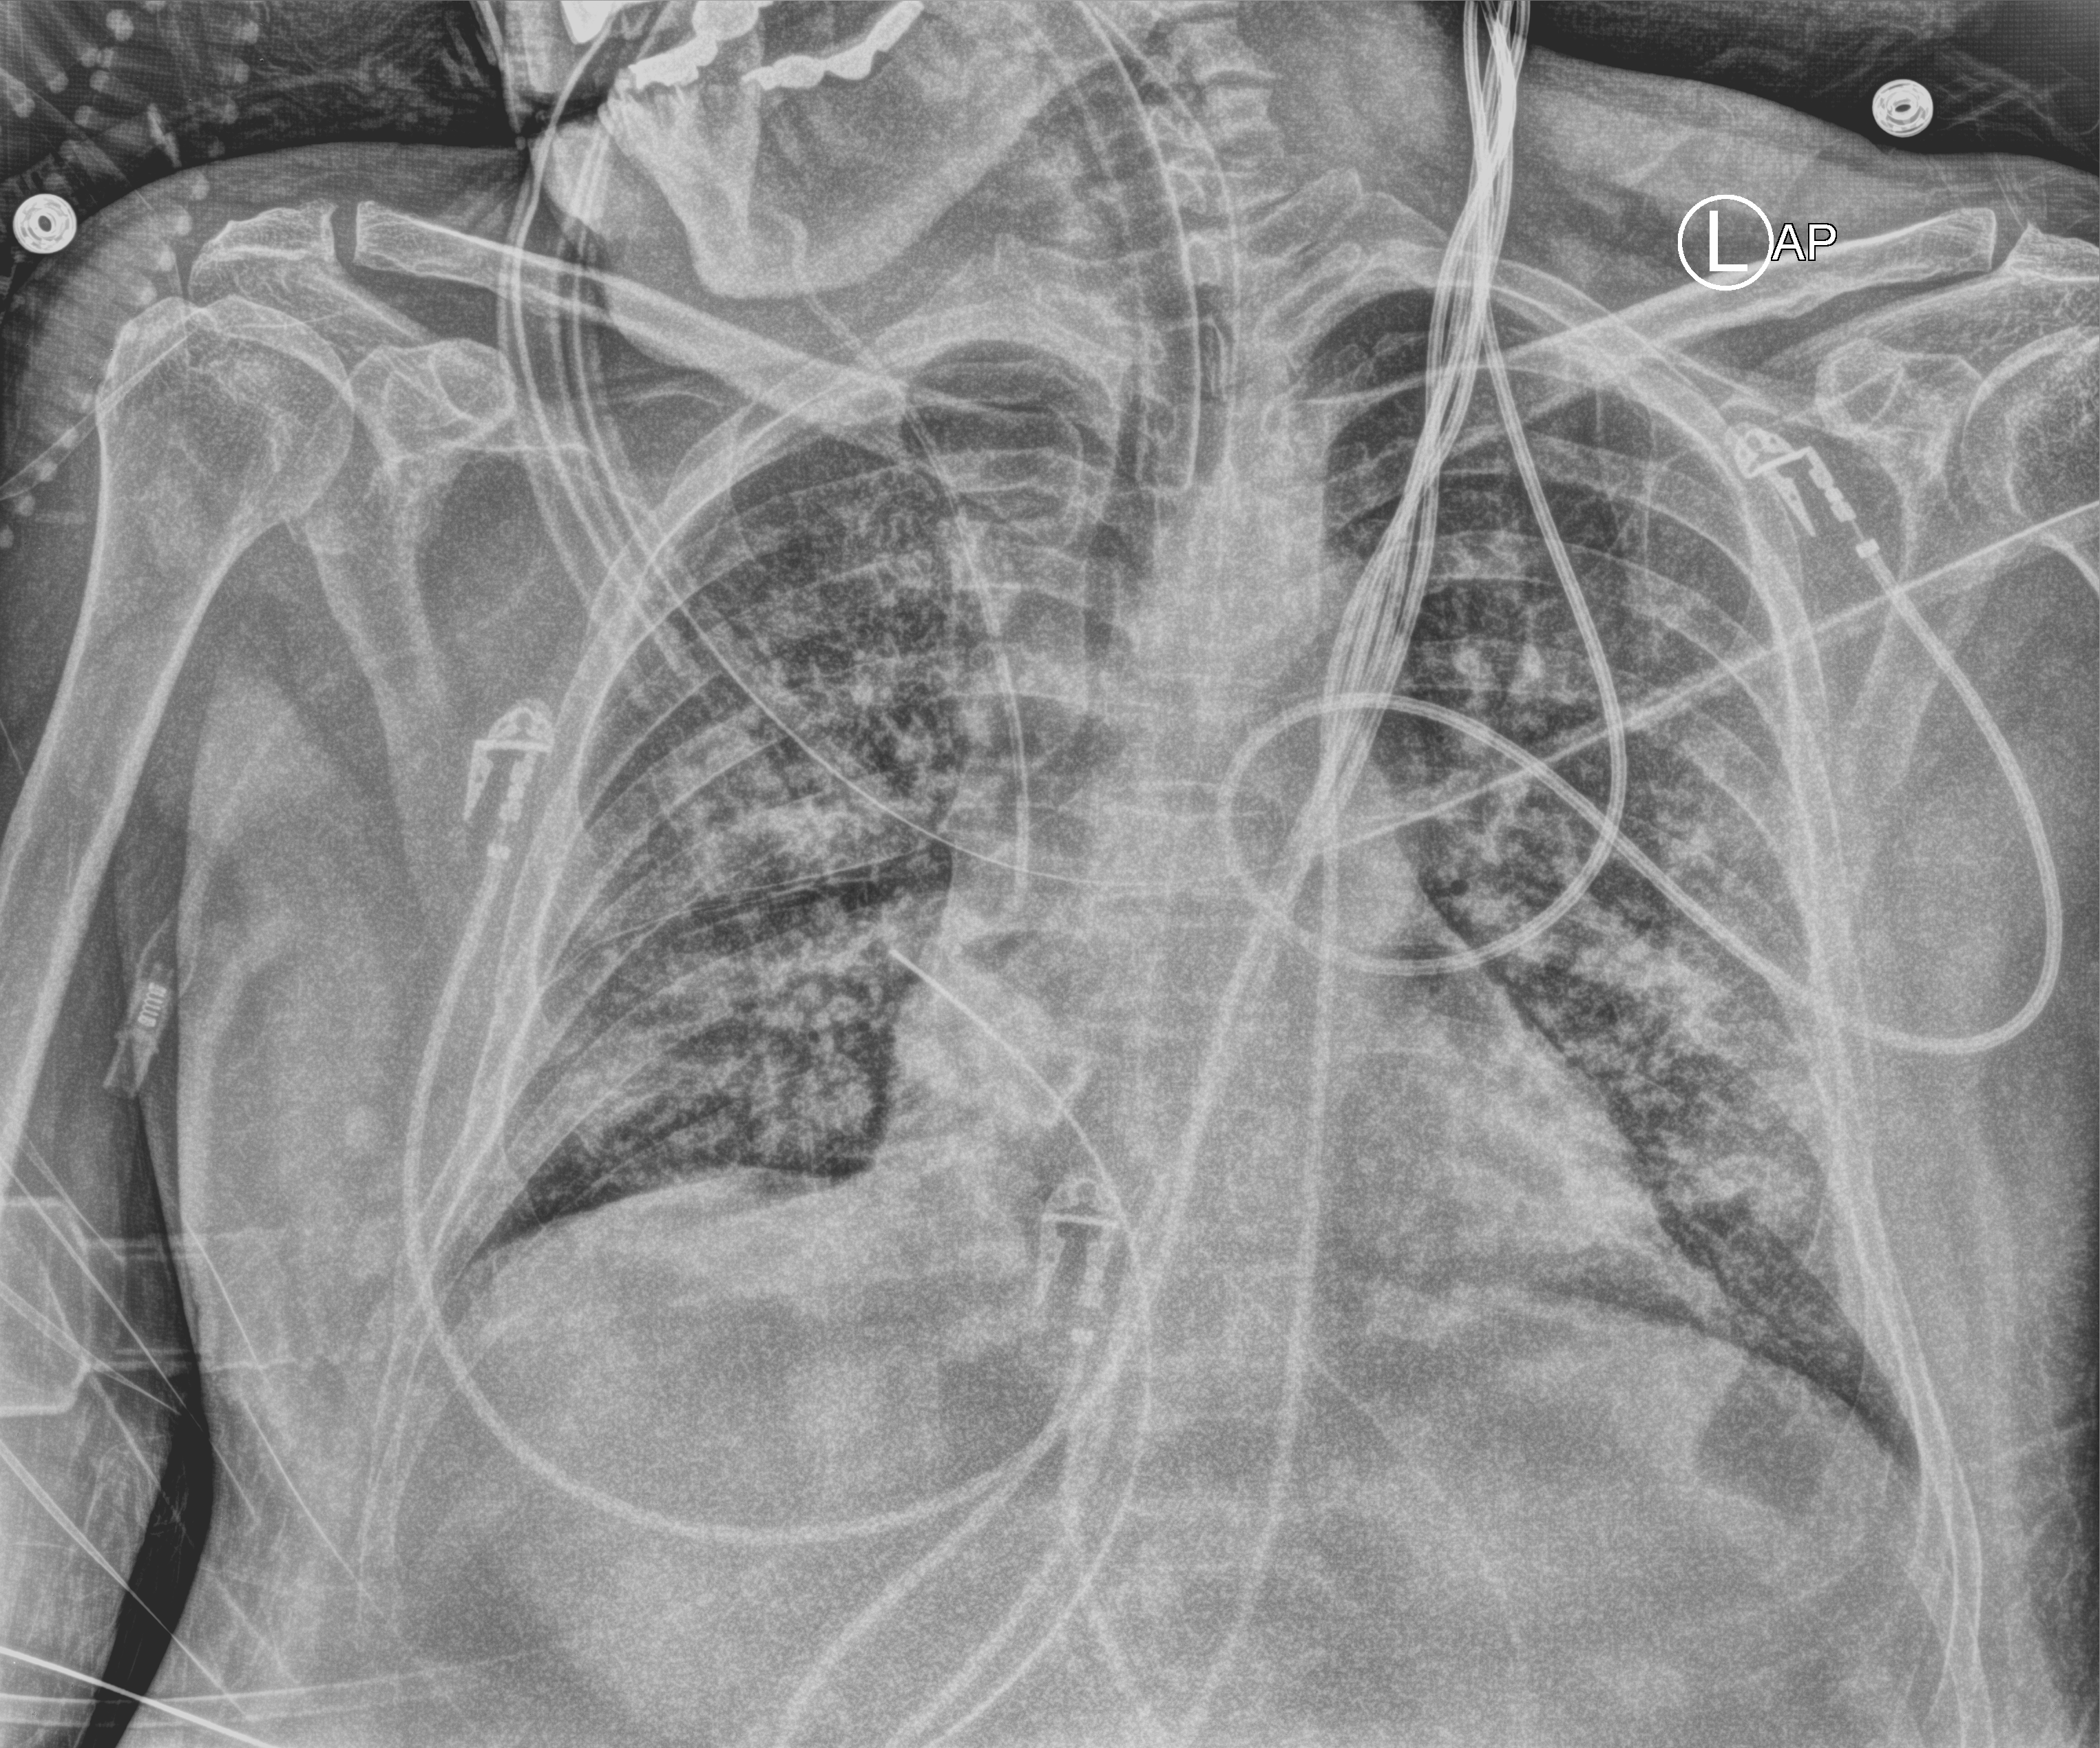
Portable chest radiograph; anteroposterior (AP) projection. Male patient hospitalised with COVID-19, age 60–74 years.
Admission-level facts for this patient (not findings on this image; timing relative to this image not recorded): length of hospital stay: 19 days; mechanically ventilated during this hospital stay: yes; admitted to intensive care during this hospital stay: yes.